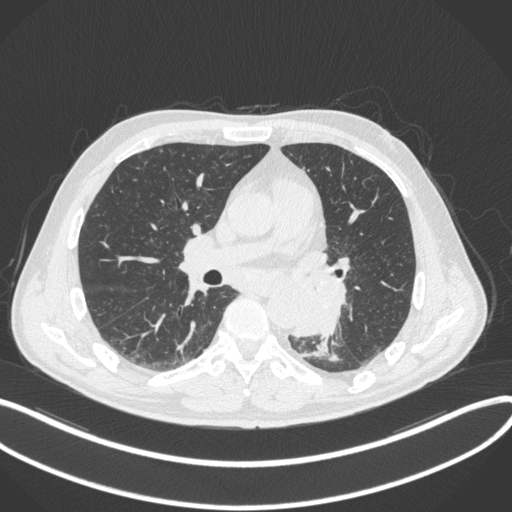
Chest CT, one axial slice; slice 180 of 328 in the series (ordered by position); reconstruction kernel B31f; 120 kVp; lung window (W 1500 / L -600 HU); 1 mm slice thickness; 512 × 512 image matrix, field of view 400 × 400 mm. Patient: male, 59 years. Case-level facts recorded for this patient, not image findings: clinical TNM (as recorded): T2a N2 M0.
Structures marked on this image (bounding box drawn by a radiologist):
- lung tumour (recorded histology: squamous cell carcinoma): bounding box <292,275,349,337> (left, top, right, bottom; pixels)